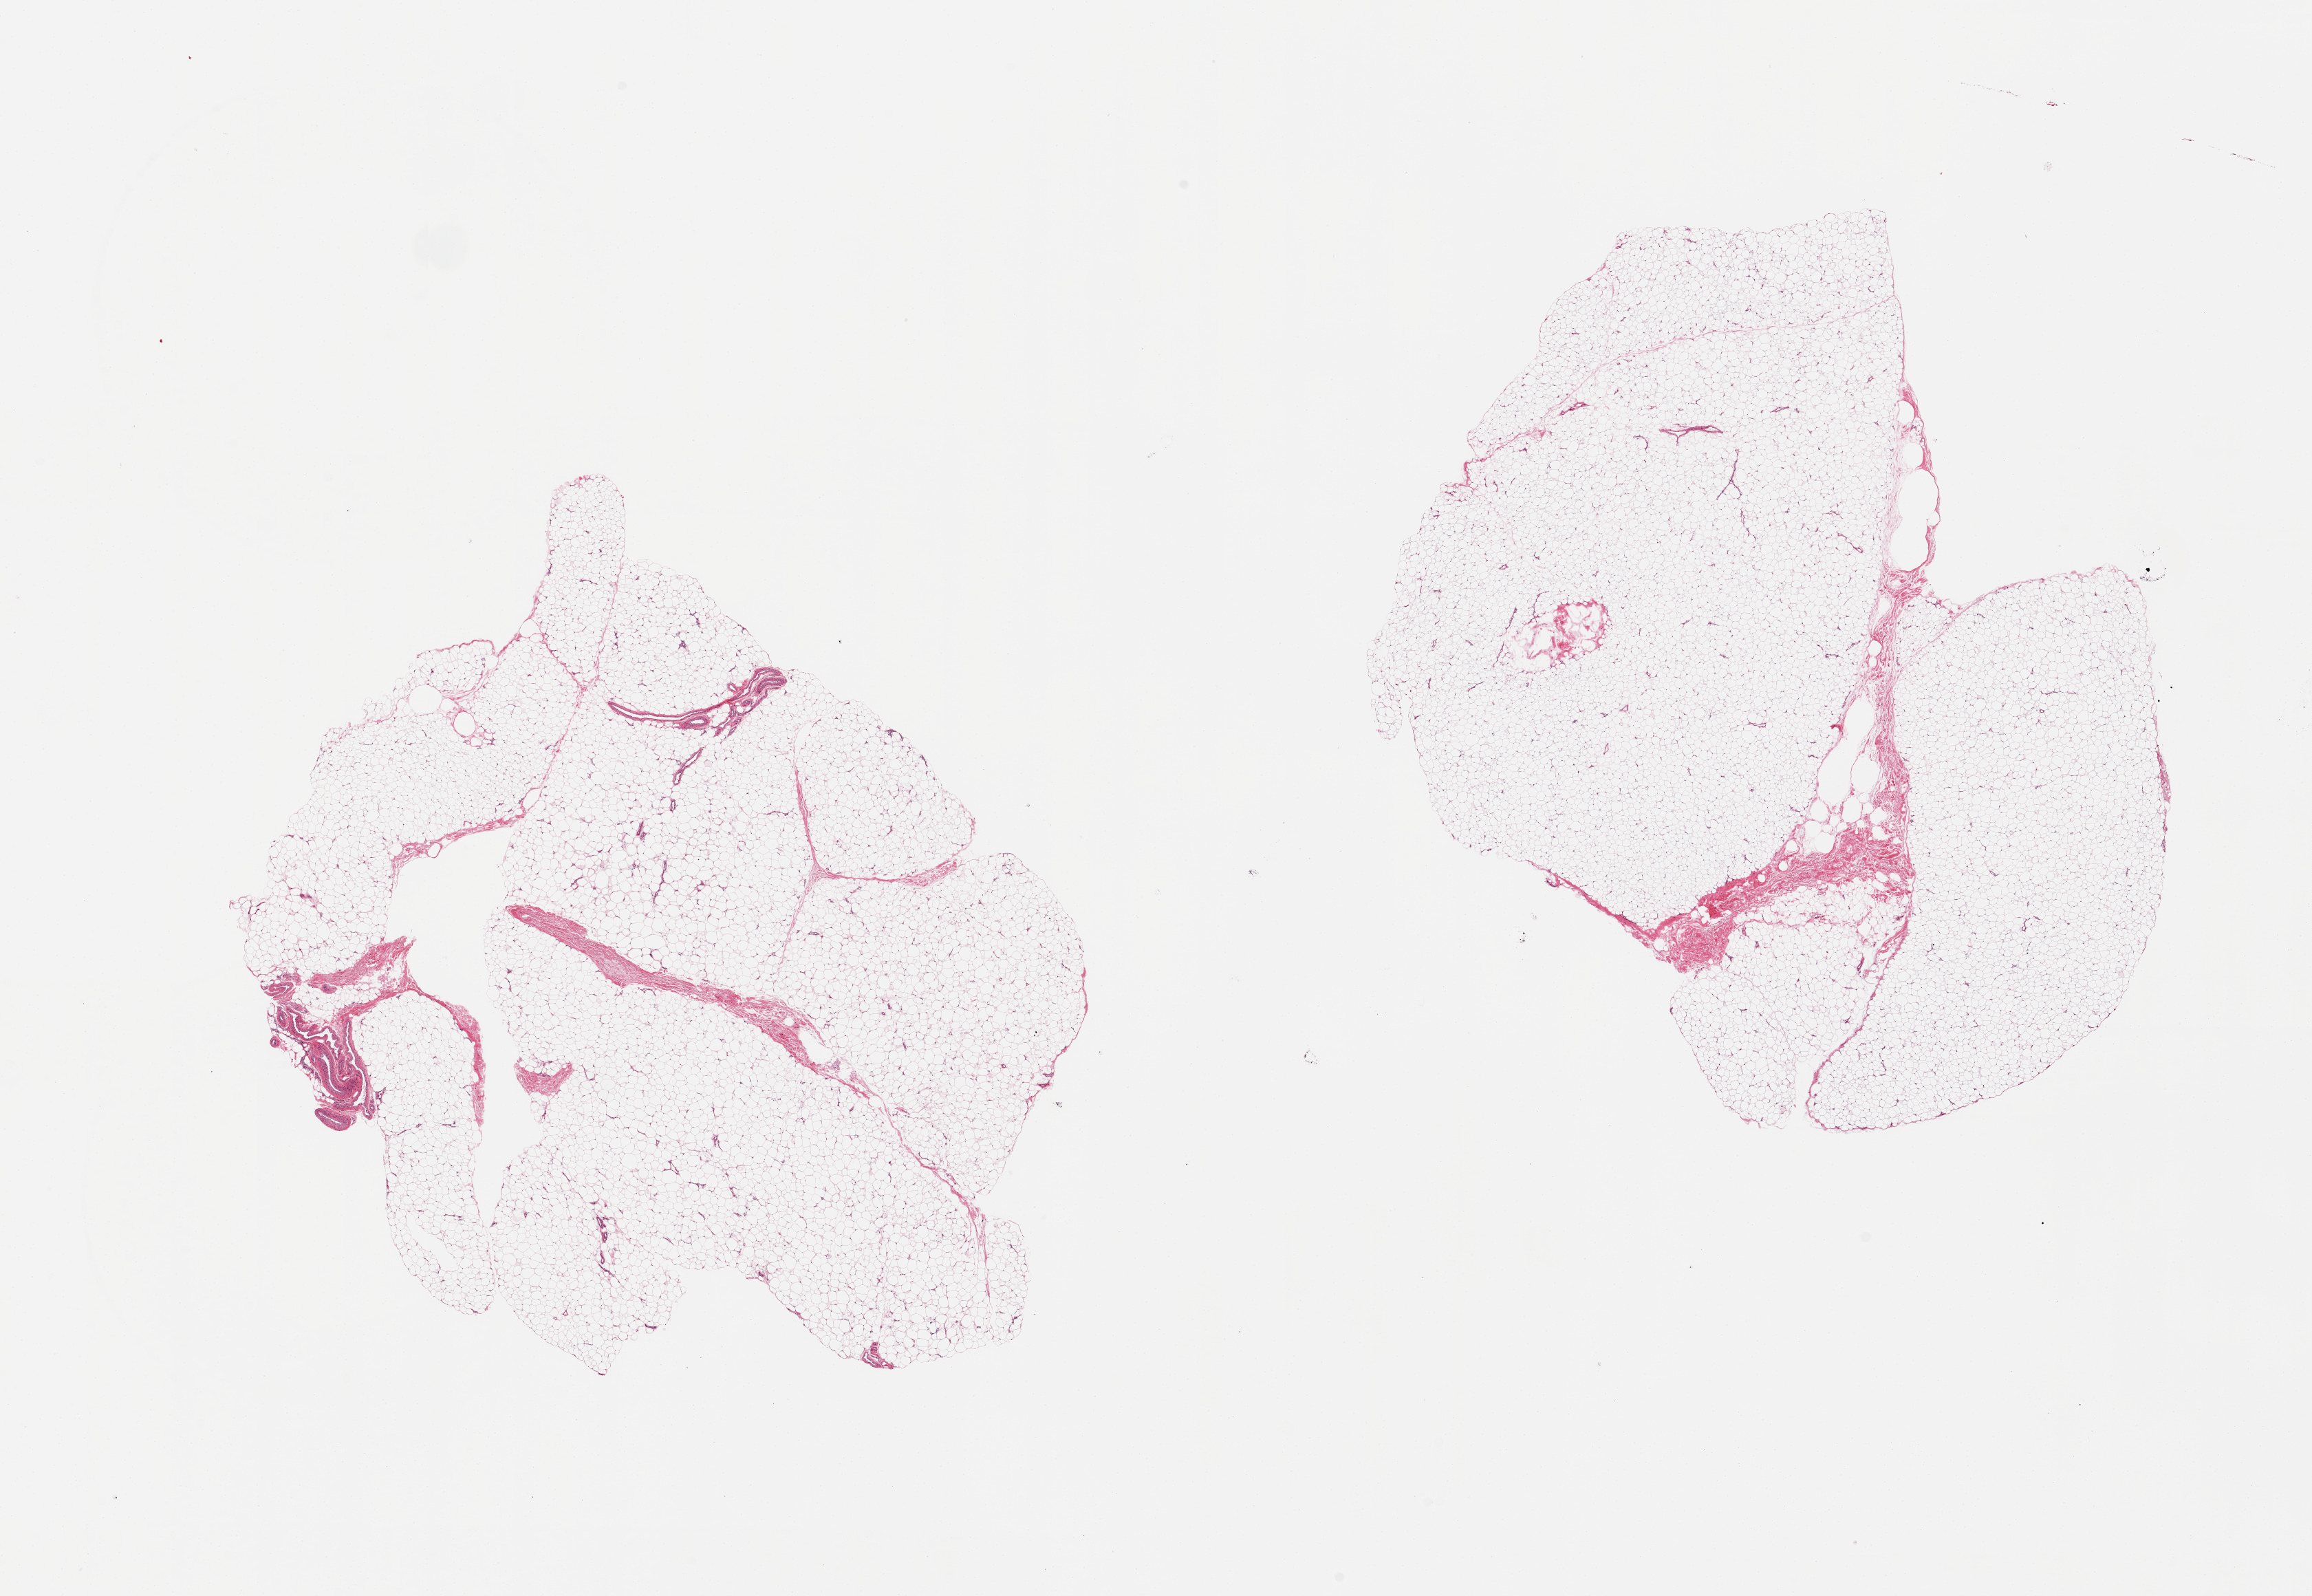
Haematoxylin and eosin whole-slide image, shown as a low-resolution overview of the whole scanned area (about 26.6 x 18.3 mm, slide scanned at 20x). PAXgene-fixed paraffin-embedded (PFPE) section. Target tissue: adipose tissue. Donor tissue sample. Donor: male.
• pathologist's review note for this sample: 2 pieces, ~5-10% fascia/vascular elements